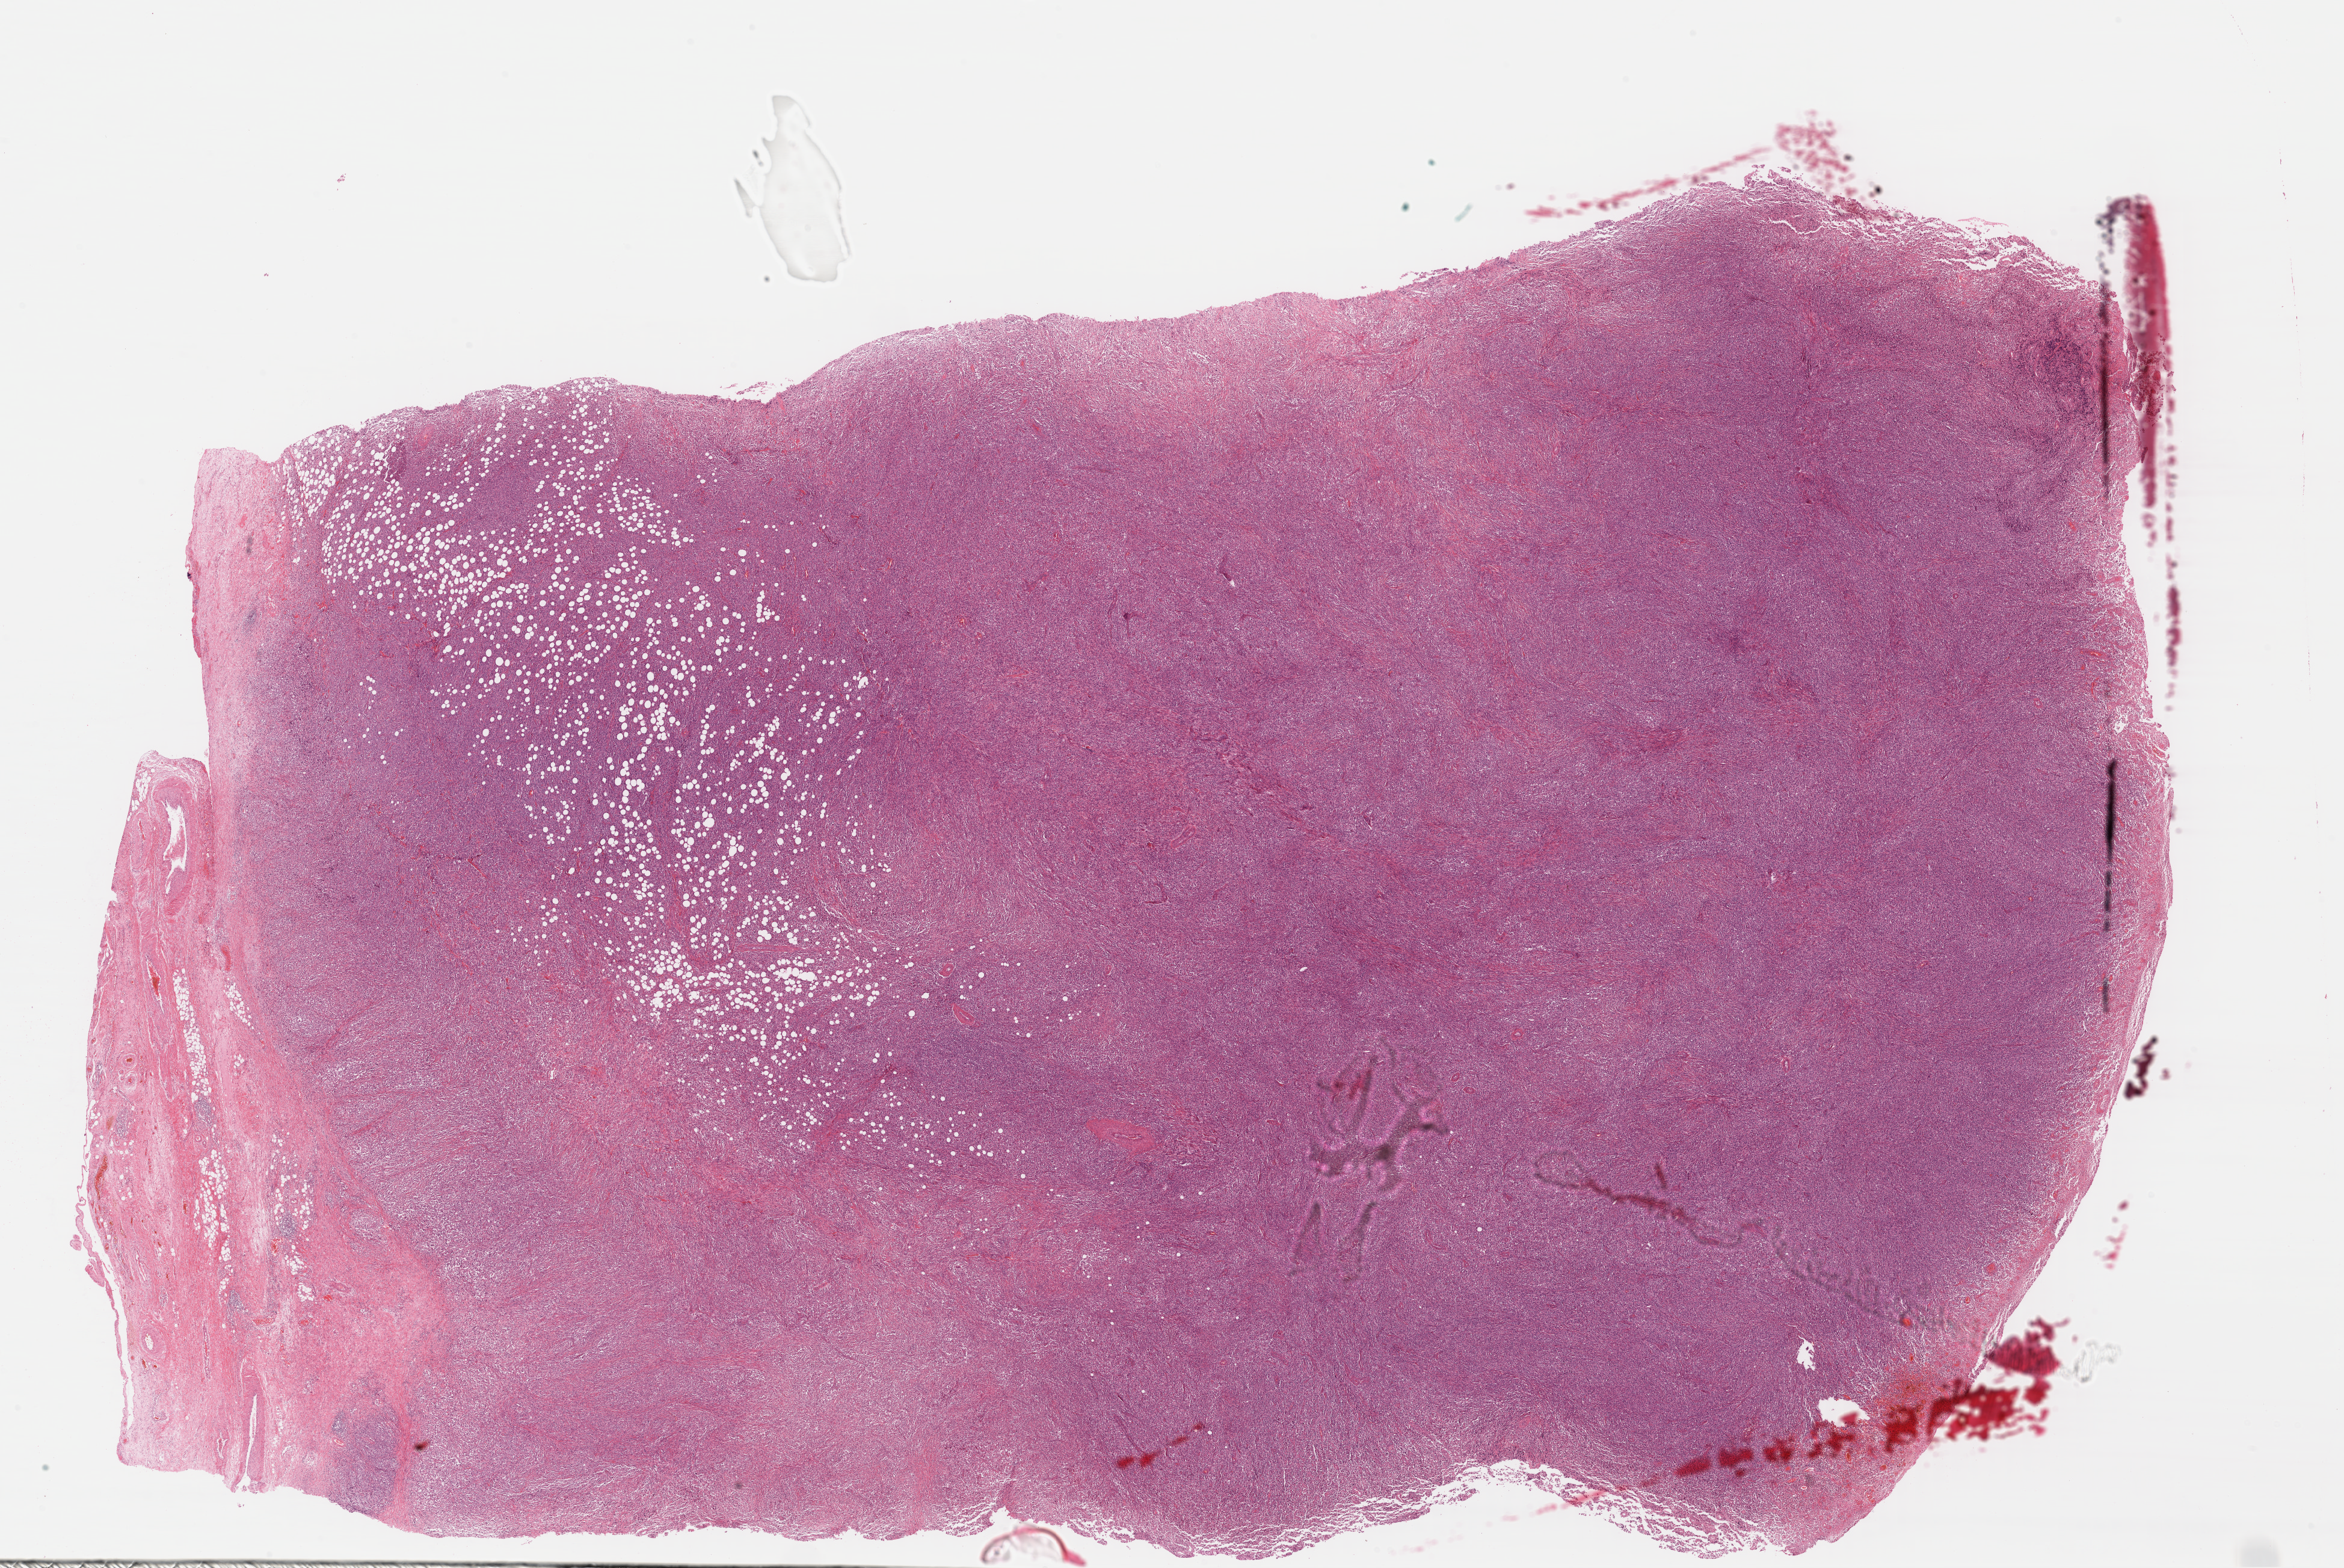
Hematoxylin and eosin (H&E) stained whole-slide image — low-resolution overview of the scanned area, about 30.6 x 20.5 mm; formalin-fixed paraffin-embedded (FFPE) diagnostic section; primary tumour sample from the lymphoid tissue. Male, age 40 years at initial diagnosis.
Pathologic diagnosis: Diffuse large B-cell lymphoma, NOS (jejunum).